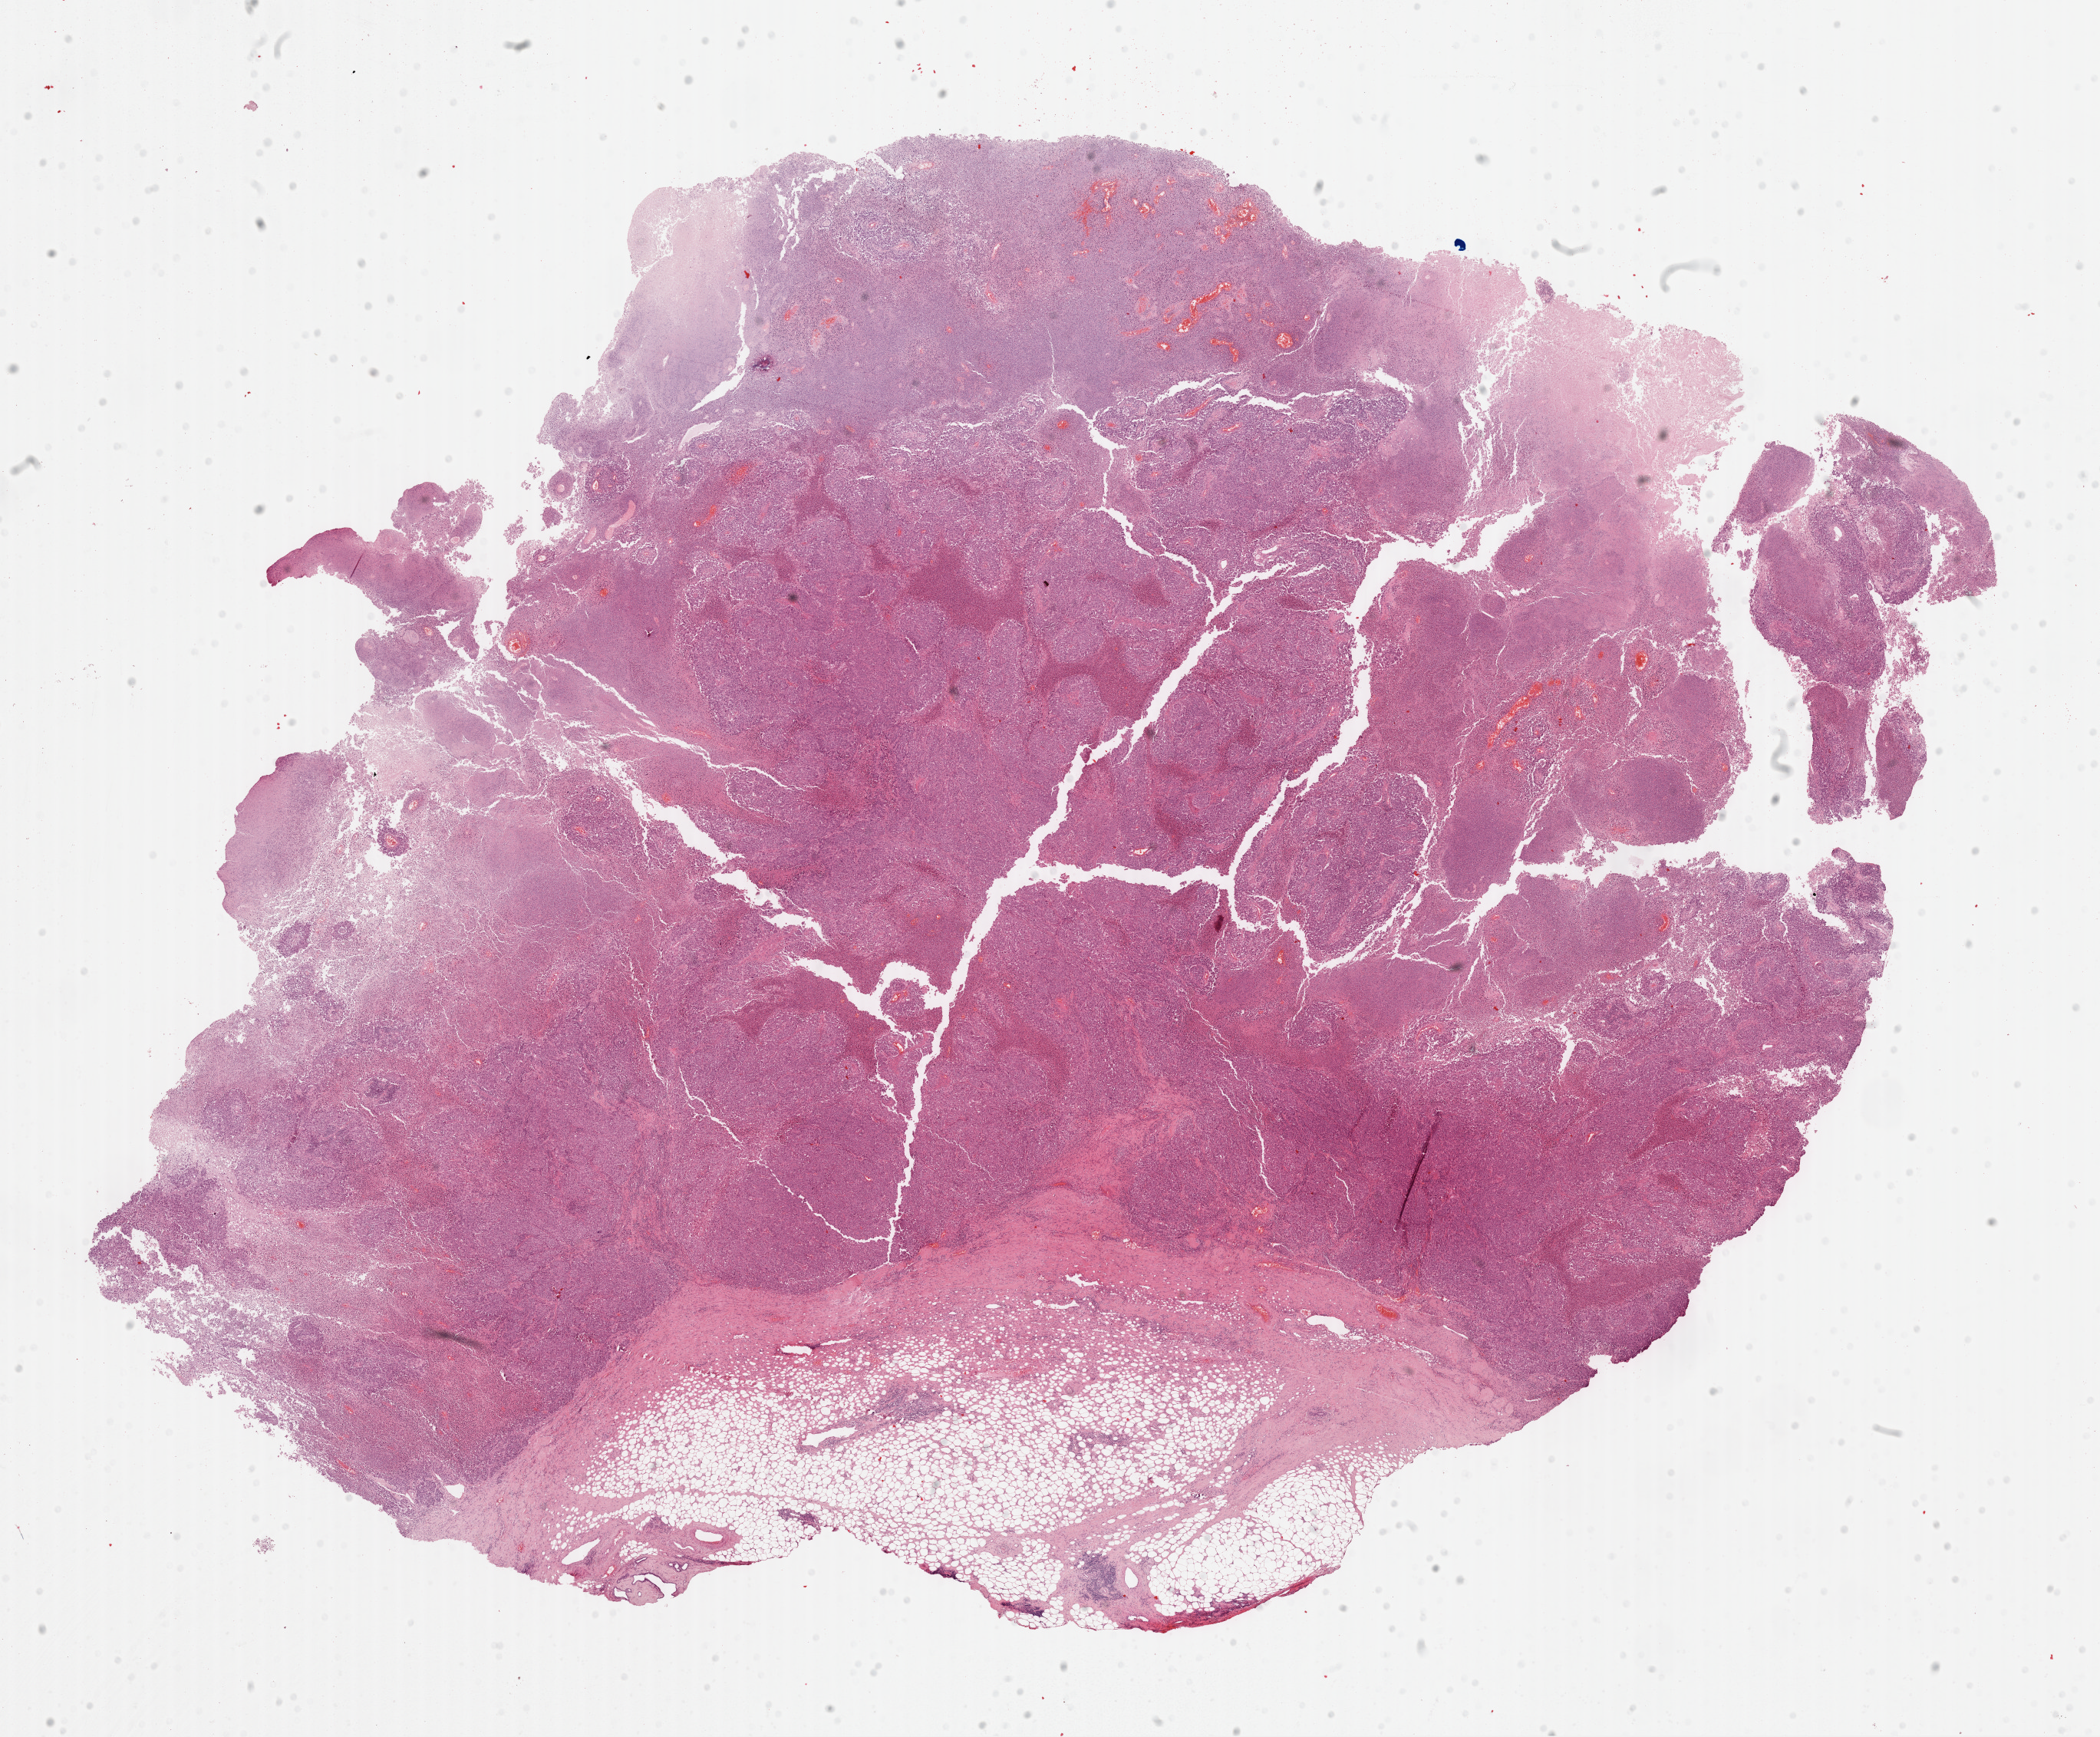
Whole-slide histology image, Hematoxylin and eosin (H&E) stained, low-resolution overview of the scanned area, about 21.6 x 17.9 mm. Formalin-fixed paraffin-embedded (FFPE) diagnostic section. Primary tumour sample from the breast. Female, age 55 years at initial diagnosis.
* histologic diagnosis: Infiltrating duct carcinoma, NOS
* lymph nodes positive (case pathology): 3 of 18 examined
* TNM: T2 N1a MX
* AJCC pathologic stage: IIB (7th edition)